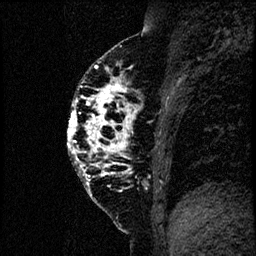
Breast MRI (dynamic contrast-enhanced), one sagittal slice; position 31 of 60 along the scan axis; dynamic contrast-enhanced study with each time point stored as its own series, time point 2 of 4 at this slice position (early post-contrast, ordered by acquisition time); 1.5 T; TE 4.2 ms, TR 17.6 ms; 2 mm slice thickness; 256 × 256 image matrix, field of view 200 × 200 mm. Female patient, age 40 years. From the clinical record (not read from this slice): setting: breast cancer imaged before/during neoadjuvant chemotherapy; receptor status: HER2-positive.
Structures marked on this image (semi-automatically segmented with operator editing):
- analysis volume of interest (the breast-tissue region the enhancement analysis was run in; not a lesion): bounding box [x1, y1, x2, y2] px = [66, 55, 185, 206]
- tumour enhancement mask (voxels above the 100 % enhancement threshold inside the analysis volume of interest): [67, 65, 134, 175]